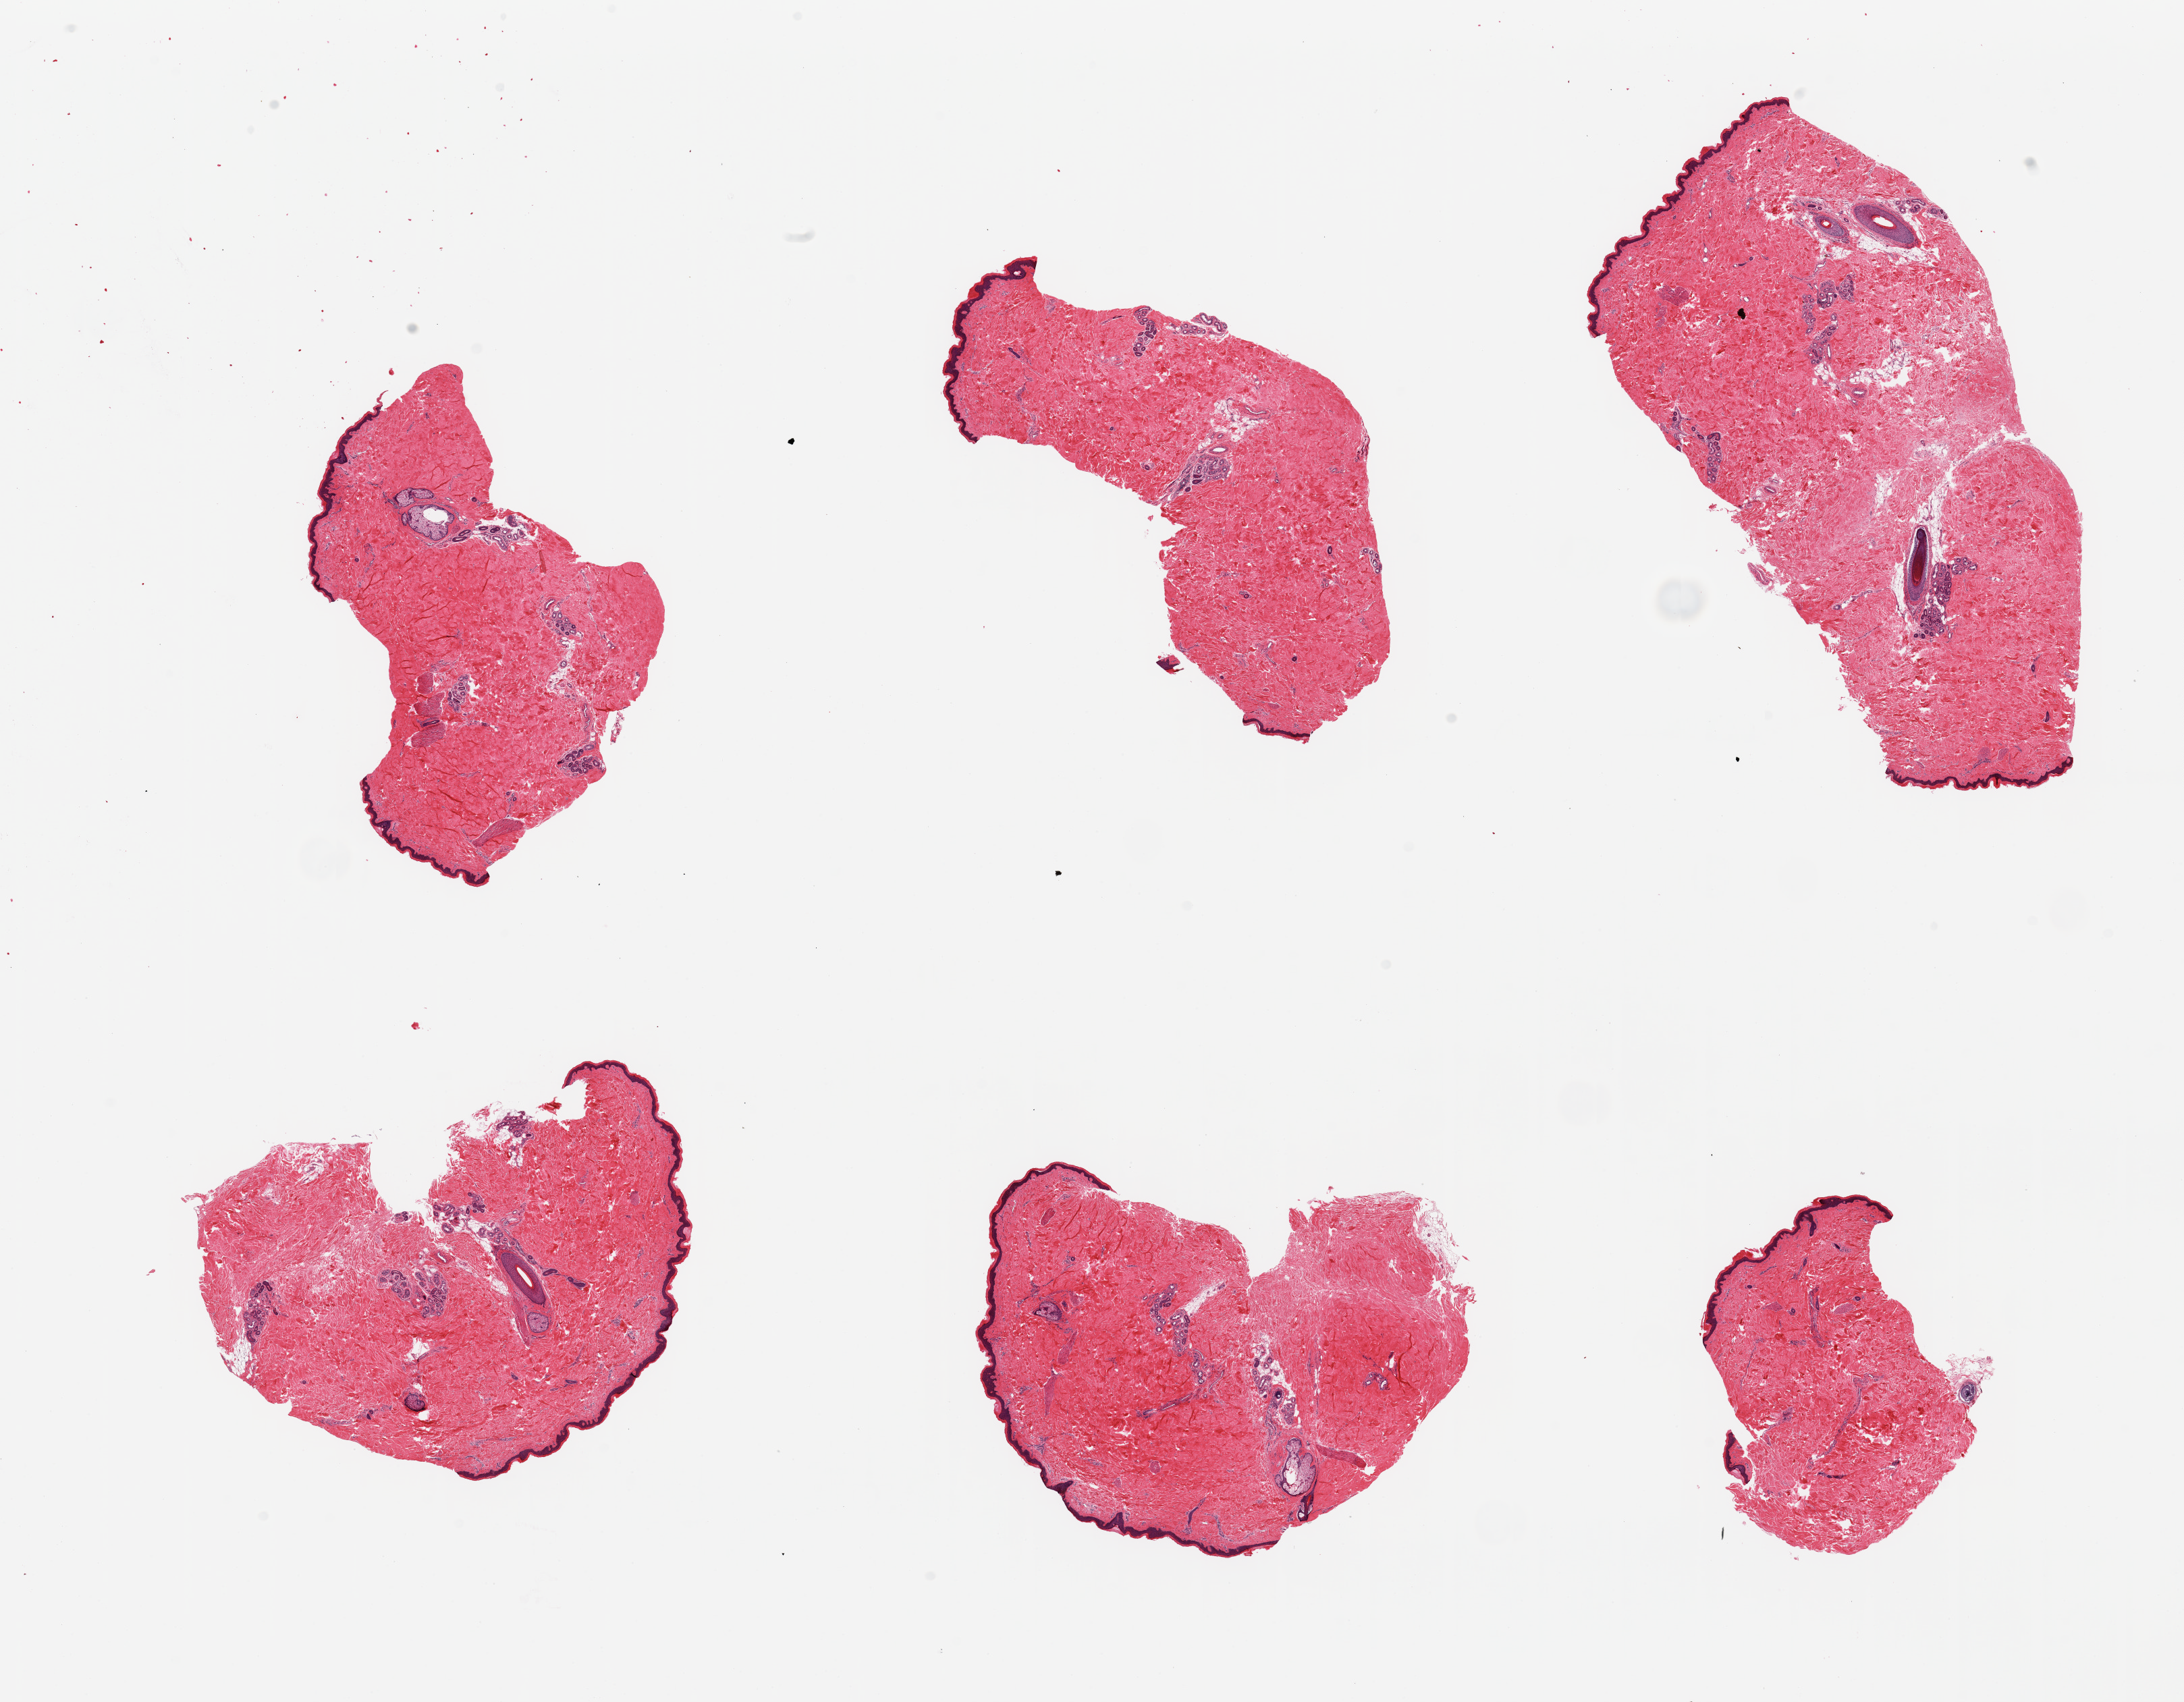
Whole-slide image, hematoxylin and eosin (H&E) stain, brightfield — a low-resolution overview of the entire scanned area, about 25.6 x 19.9 mm (acquisition: 20x scan). PAXgene-fixed, paraffin-embedded tissue. Target tissue: skin of lower leg. Tissue donor sample. Donor: male.
Pathologist's review note for this sample: 6 pieces; well trimmed; <5% intradermal fat.